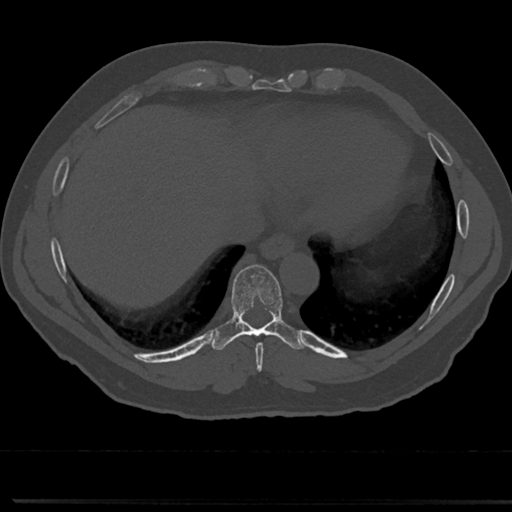
CT including the spine, one axial slice; position 312 of 817 along the scan axis; reconstruction kernel Br40s/3; 120 kVp; bone window (W 1800 / L 400 HU); 0.5 mm slice thickness; 512 × 512 image matrix, field of view 355 × 355 mm. Male patient, age 61 years. From the clinical record (not read from this slice): primary cancer: prostate.
Annotated regions visible in this slice (semi-automatically segmented with operator editing):
- T8 vertebra: bounding box [x1, y1, x2, y2] px = [231, 270, 290, 353]
- T9 vertebra: [233, 267, 282, 328]